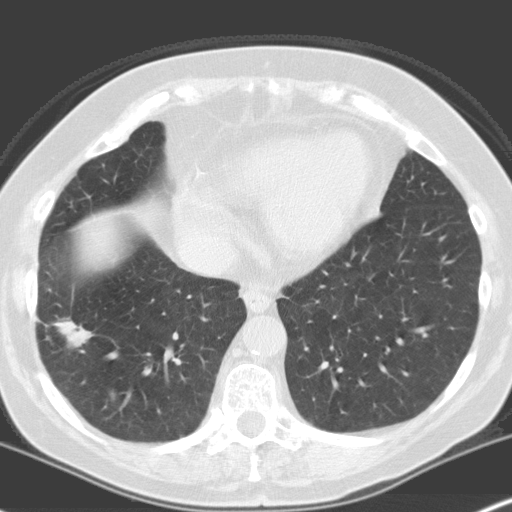
Low-dose screening chest CT, one axial slice; position 61 of 160 along the scan axis; 120 kVp; lung window (W 1500 / L -600 HU); 512 × 512 image matrix, field of view 316 × 316 mm.
Structures marked on this image (manually delineated by an expert):
- lesion 1 (tumor, lower lobe of right lung): box from (x=55, y=318) to (x=92, y=348) px